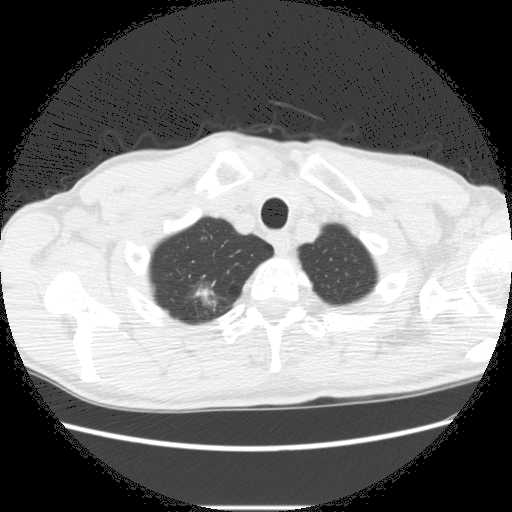
Axial slice from a low-dose chest CT screening exam; second annual screen; lung window (W 1500 / L -600 HU); standard (soft-tissue) reconstruction kernel (STANDARD); slice 23 of 282 in the series; 512 × 512 image matrix. Male, age 66 years at enrolment. Former smoker at enrolment.
Lesion marked by an expert reader, bounding box (x1, y1, x2, y2) in pixels: (171, 276, 234, 327). The screening reader recorded 5 non-calcified nodules or masses ≥4 mm on this exam (right lower lobe, right upper lobe, right upper lobe, right upper lobe, left lower lobe); which of them this box marks is not recorded. Lung cancer was diagnosed 75 days after this screen: adenocarcinoma, NOS, right upper lobe, undifferentiated (G4), stage IA (AJCC 6th edition), 20 mm at pathology.